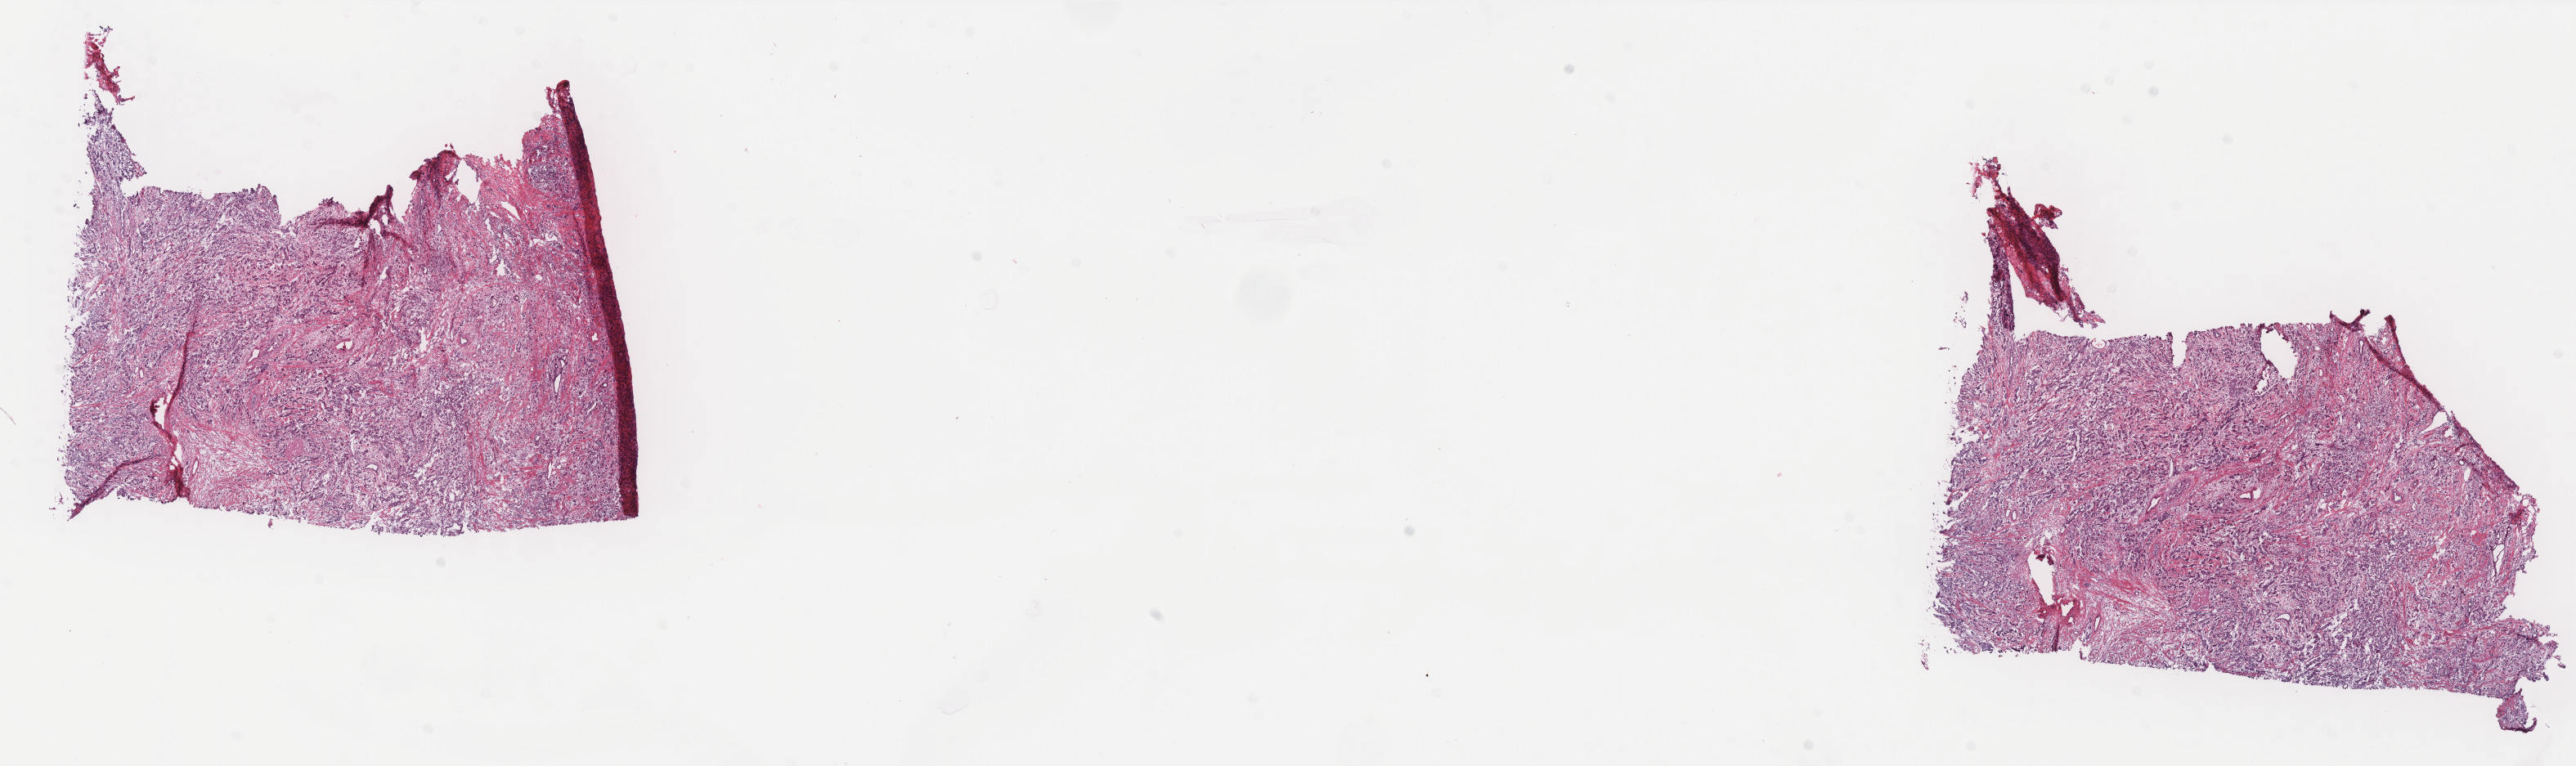
Hematoxylin and eosin (H&E) stained whole-slide image — shown as a low-resolution overview of the whole scanned area (about 25.3 x 7.5 mm, acquisition: 40x scan). Frozen section from the bottom of the tissue portion. Breast, primary tumour sample. Female patient; age at initial diagnosis 34 years. Pathologist review of this section (percent, as recorded): tumour cells 85%, tumour nuclei 80%, normal cells 2%, stromal cells 12%, necrosis 1%. Inflammatory infiltration, as recorded: lymphocyte infiltration 10%, monocyte infiltration 0%, neutrophil infiltration 0%.
* AJCC pathologic stage: IIIA (6th edition)
* laterality: right
* diagnosis: Infiltrating duct carcinoma, NOS